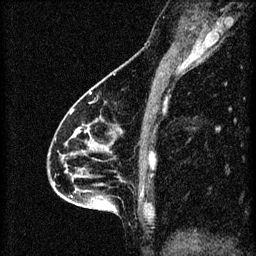
Breast MRI (dynamic contrast-enhanced), one sagittal slice. 3 images stored at this slice position (order not interpretable as contrast timing). 1.5 T. TE 4.2 ms, TR 8.2 ms. 2 mm slice thickness. 256 × 256 image matrix. Female patient, age 46 years.
Annotated regions visible in this slice (semi-automatic segmentation, software-assisted and operator-edited):
- analysis volume of interest (the breast-tissue region the enhancement analysis was run in; not a lesion): bounding box <55,114,148,209> (left, top, right, bottom; pixels)
- tumour enhancement mask (voxels above the 70 % enhancement threshold inside the analysis volume of interest): <76,128,142,195>